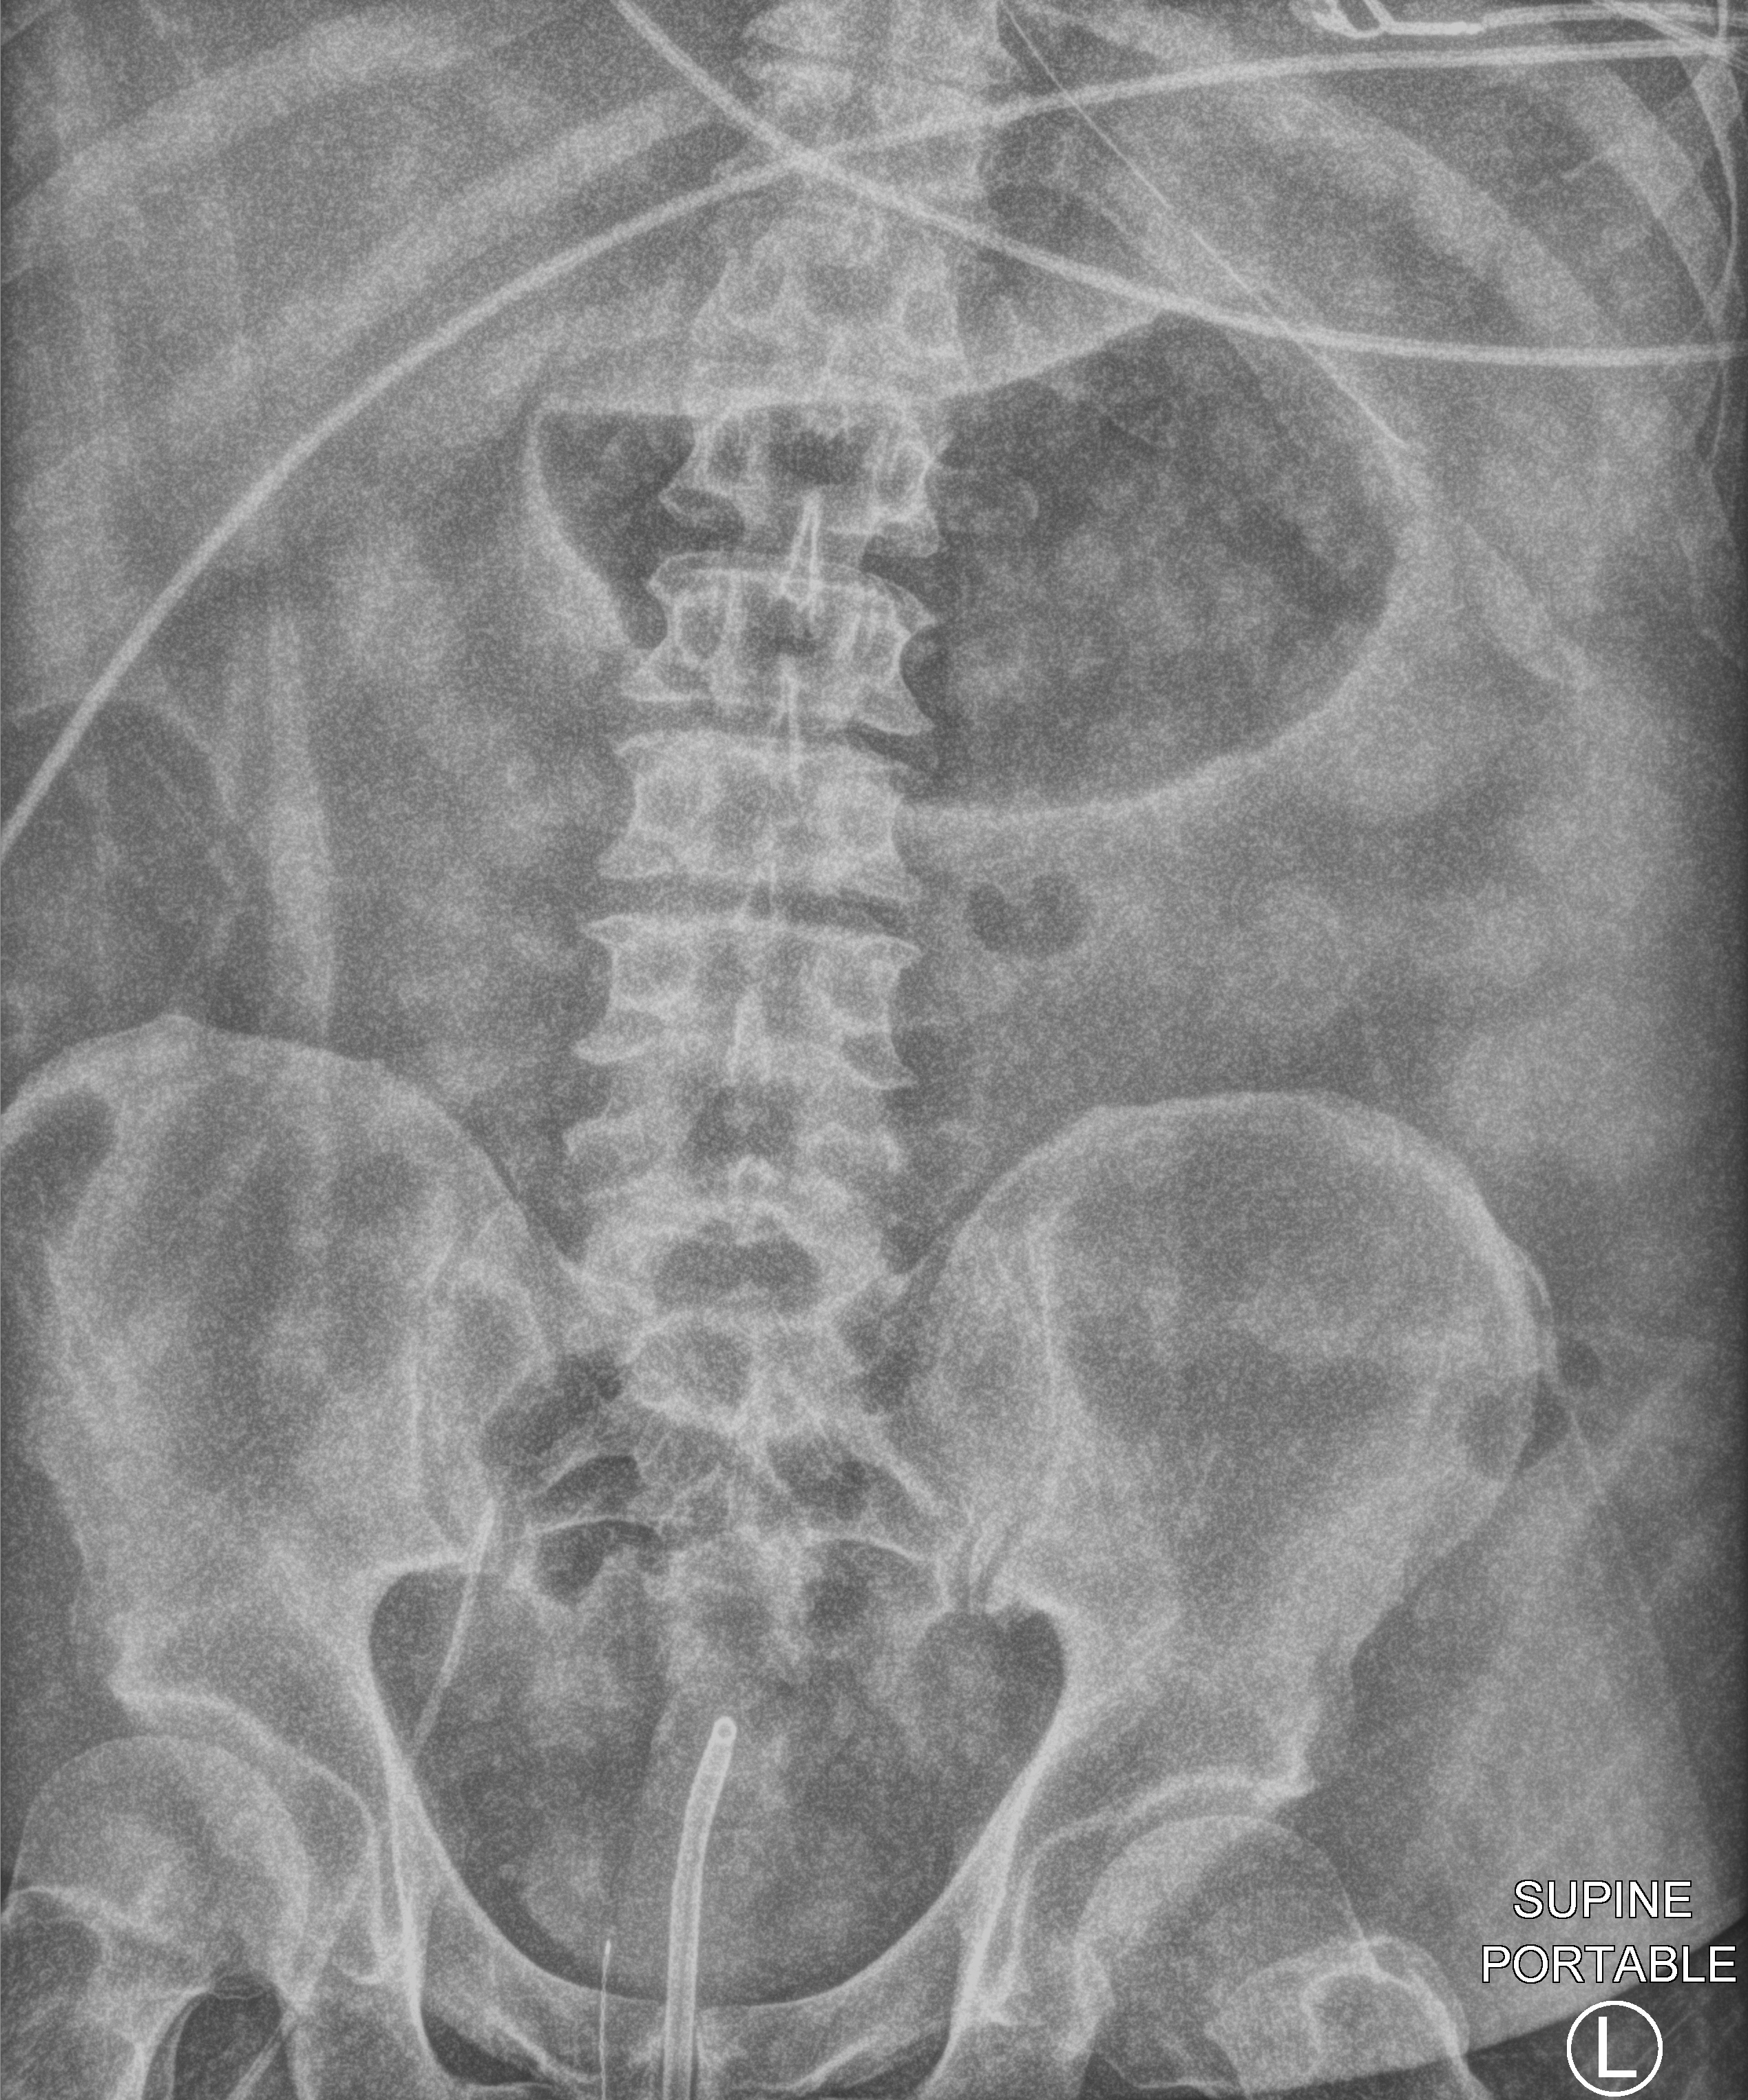
Bedside abdomen radiograph (computed radiography); anteroposterior (AP) projection. Patient hospitalised with COVID-19; male, aged 18–59 years.
From the hospital-stay record, not from the radiograph (when in the stay this image was taken is not recorded): admitted to intensive care during this hospital stay: yes; mechanically ventilated during this hospital stay: yes; length of hospital stay: 28 days.